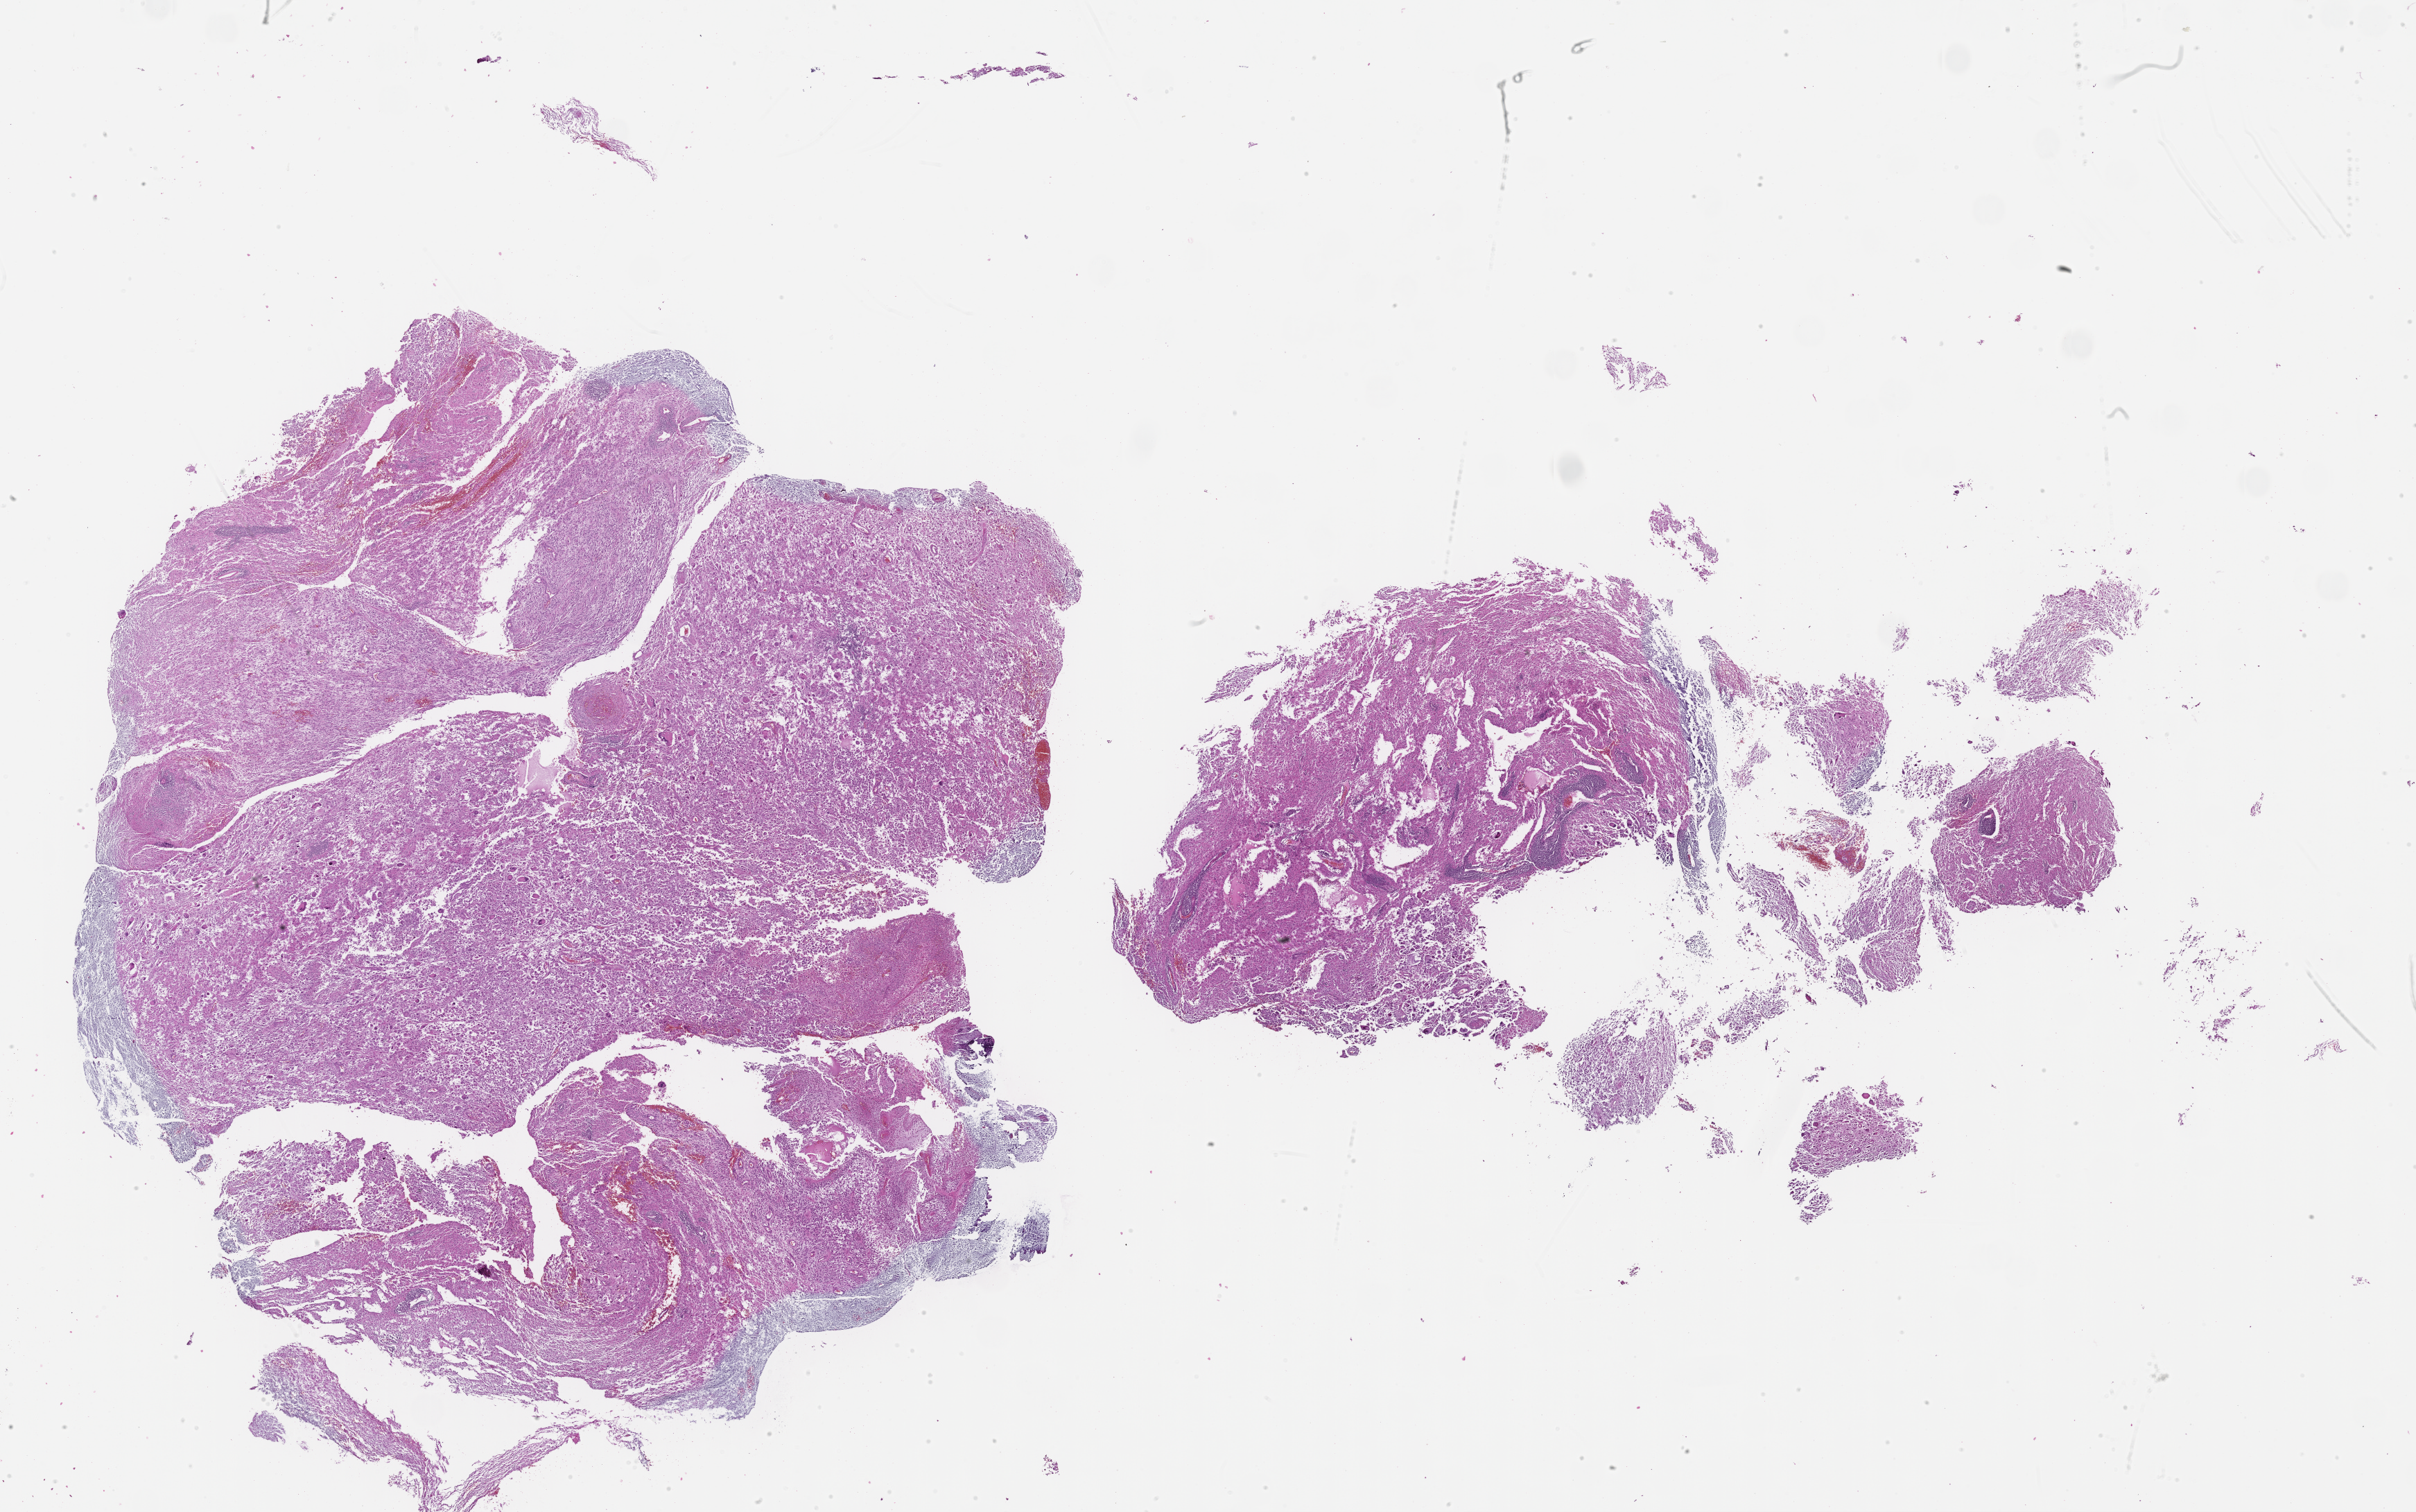
H&E-stained whole-slide image — whole scanned area (about 28.3 x 17.7 mm) shown as a low-resolution overview; formalin-fixed paraffin-embedded (FFPE) diagnostic section; brain, primary tumour sample. Patient: female, age at initial diagnosis 51 years.
Diagnosis: Glioblastoma.